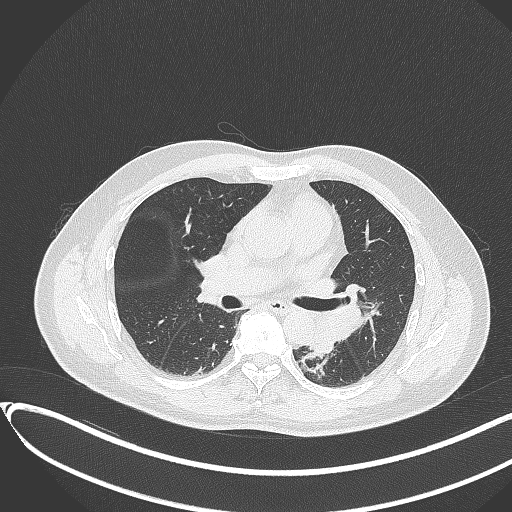
Chest CT, one axial slice. Lung window (W 1500 / L -600 HU). 512 × 512 image matrix, field of view 400 × 400 mm. Patient: male, 54 years. Case-level facts recorded for this patient, not image findings: clinical TNM (as recorded): T3 N0 M0.
Structures marked on this image (bounding box drawn by a radiologist):
- lung tumour (recorded histology: squamous cell carcinoma): box from (x=311, y=325) to (x=336, y=355) px